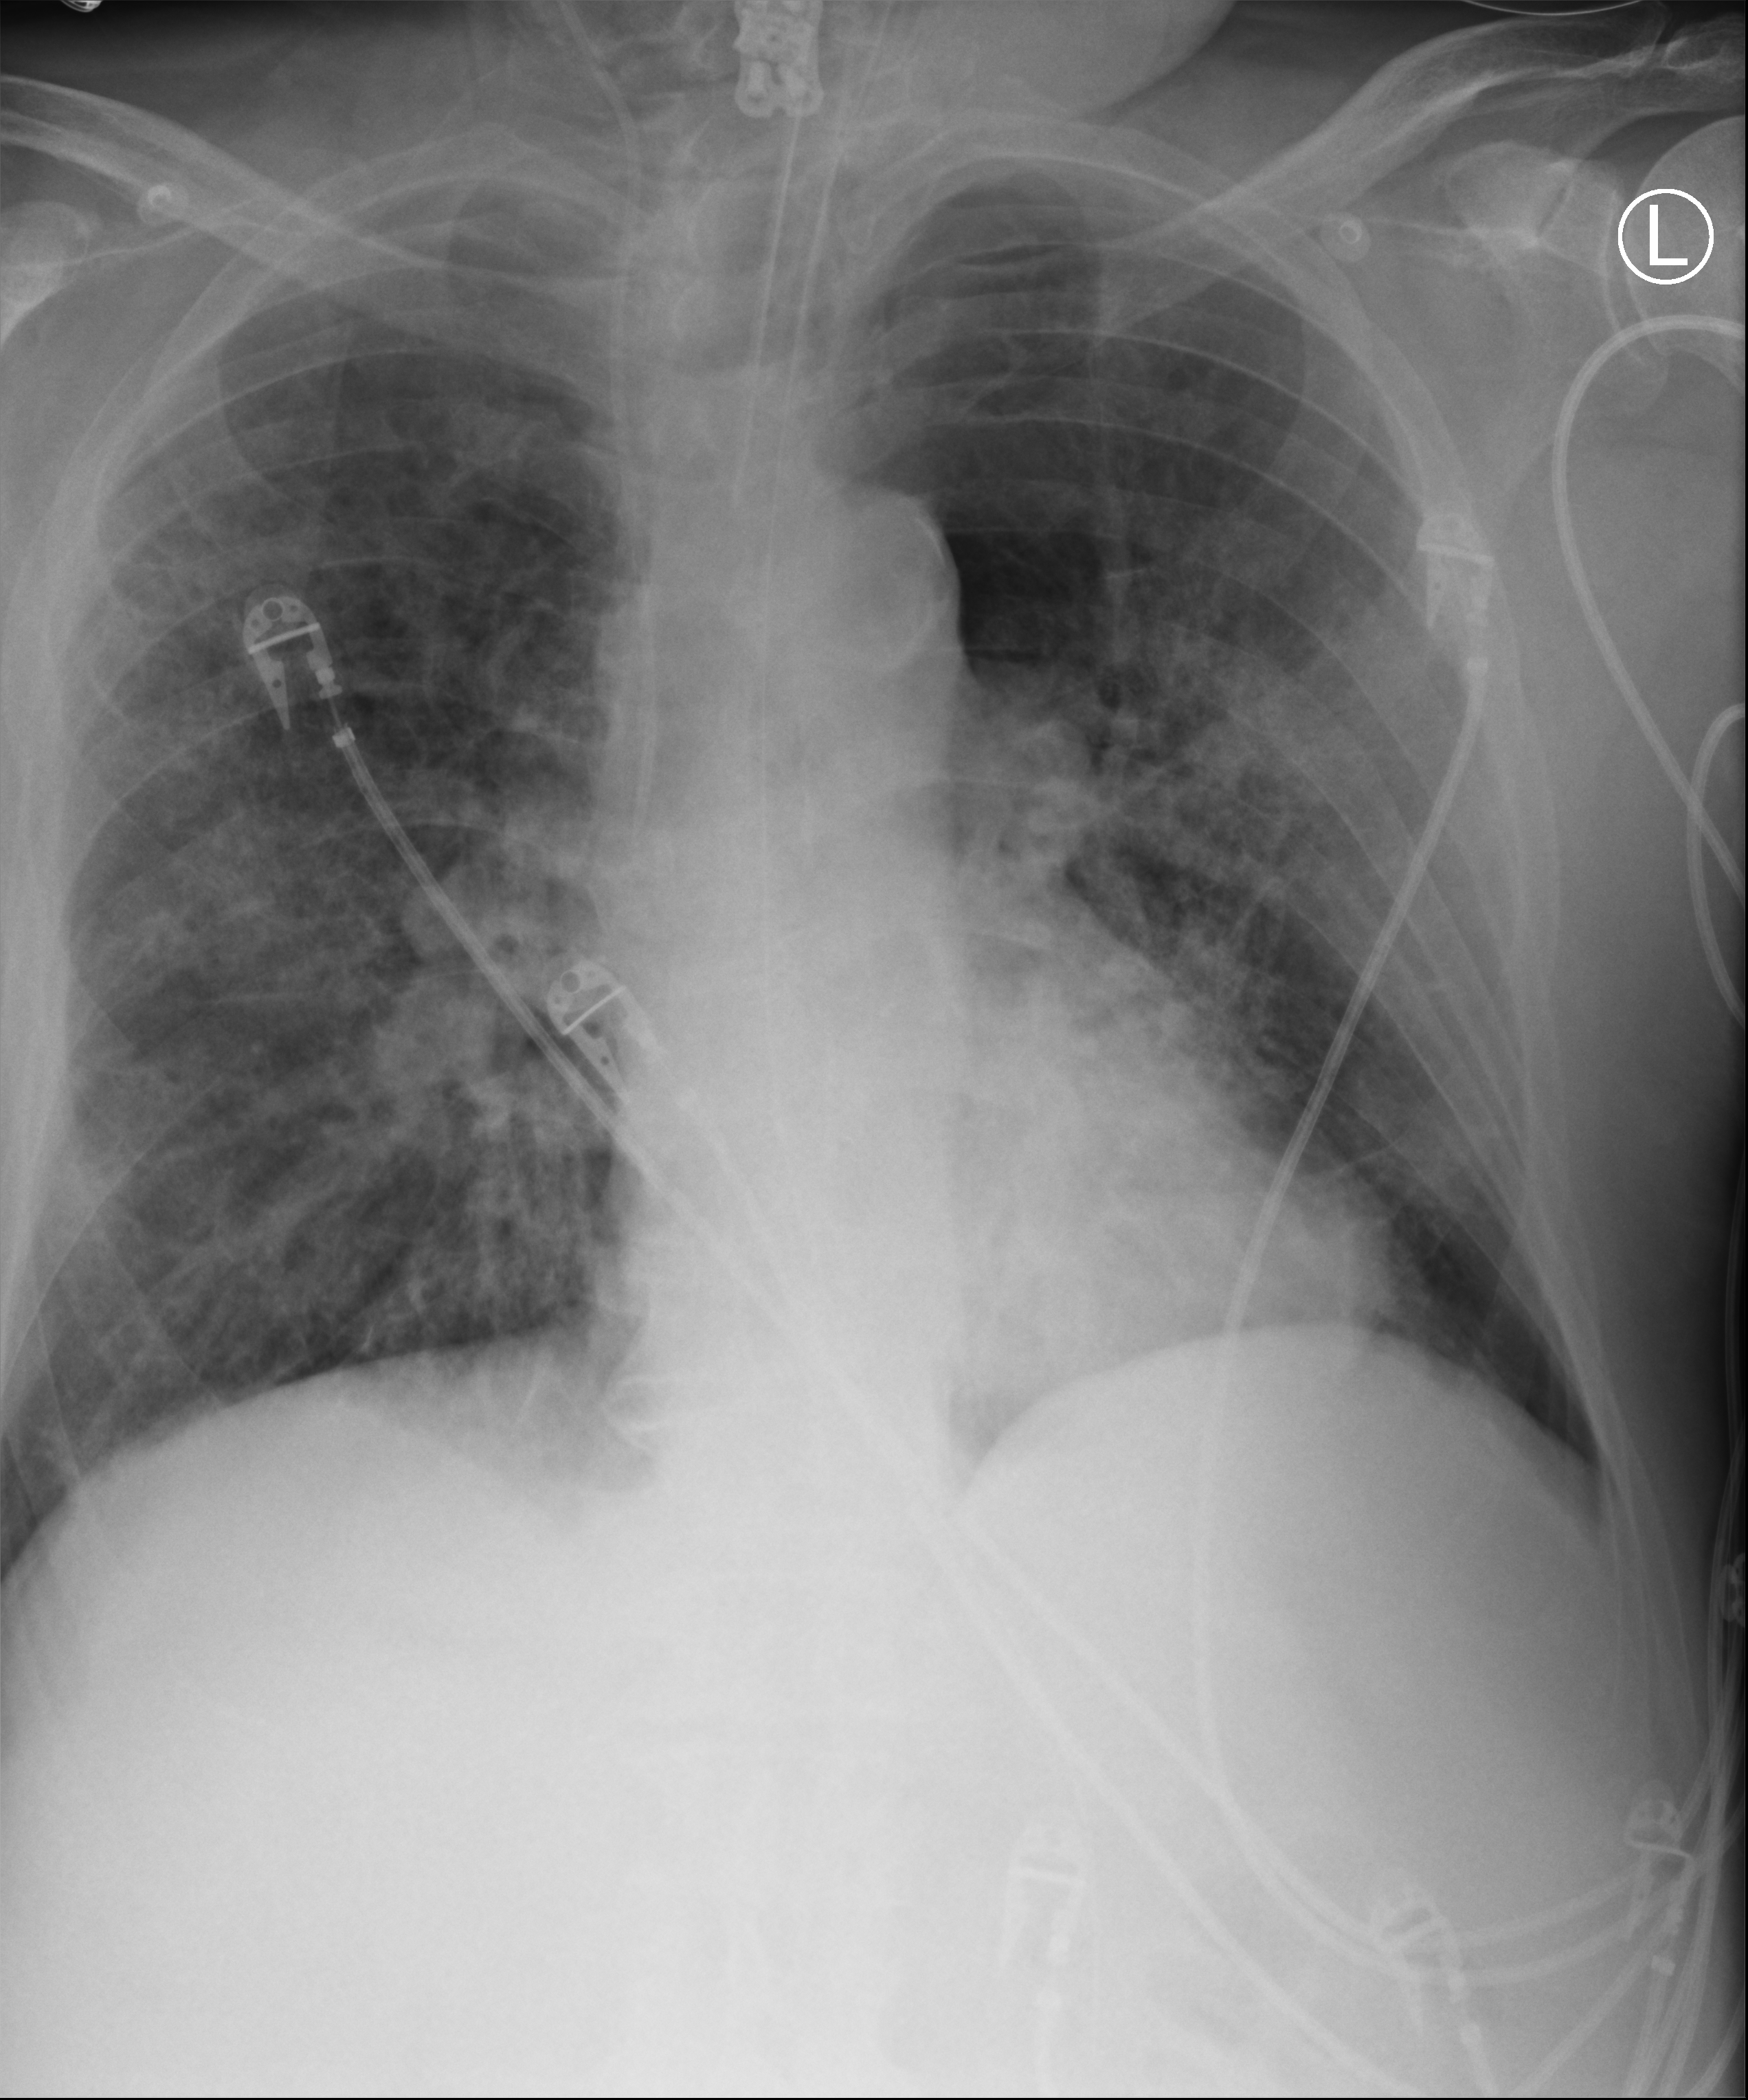
Portable chest radiograph. Patient hospitalised with COVID-19; male, aged 75–90 years.
From the hospital-stay record, not from the radiograph (when in the stay this image was taken is not recorded):
- length of hospital stay: 26 days
- admitted to intensive care during this hospital stay: yes
- mechanically ventilated during this hospital stay: yes